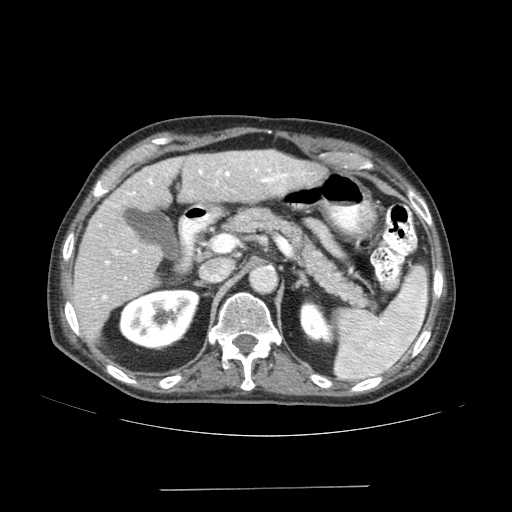
Contrast-enhanced abdominal CT (liver protocol), one axial slice; position 92 of 192 along the scan axis; reconstruction kernel SOFT; 120 kVp; soft-tissue window (W 400 / L 40 HU); 2.5 mm slice thickness; 512 × 512 image matrix. Case-level facts recorded for this patient, not image findings: diagnosis: hepatocellular carcinoma (patient treated with transarterial chemoembolisation; whether this scan precedes or follows treatment is not stated here); TNM stage (as recorded): Stage-IVA; Child-Pugh class: A; tumour differentiation: poorly differentiated; tumour nodularity: uninodular.
Structures marked on this image (semi-automatically segmented with operator editing):
- liver parenchyma outside the tumour (the mass and vessels are separate outlines, so this box may not span the whole liver): bounding box (x1, y1, x2, y2) in pixels: (72, 150, 324, 340)
- liver vessels: (100, 158, 304, 300)